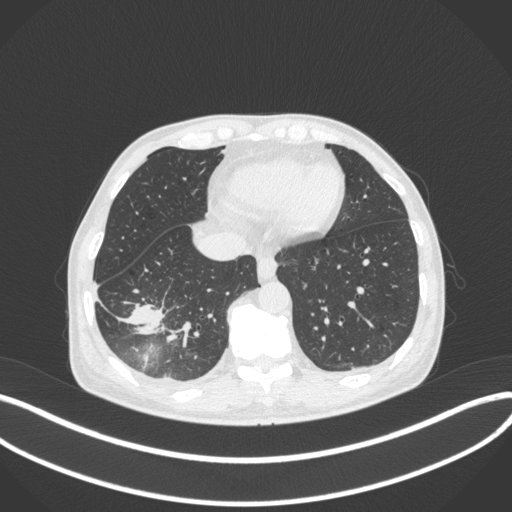
Chest CT, one axial slice. Slice 101 of 385 in the series (ordered by position). Reconstruction kernel B31f. Lung window (W 1500 / L -600 HU). 1 mm slice thickness. 512 × 512 image matrix, field of view 400 × 400 mm. Patient: male, 64 years. Case-level facts recorded for this patient, not image findings: clinical TNM (as recorded): T3 N0 M0; histopathological grade: G2-3.
Structures marked on this image (bounding box drawn by a radiologist):
- lung tumour (recorded histology: adenocarcinoma): box from (x=119, y=289) to (x=165, y=343) px